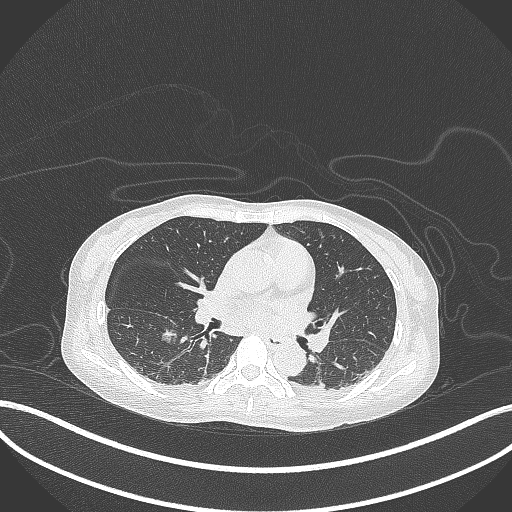
Chest CT, one axial slice. Slice 161 of 261 in the series (ordered by position). Reconstruction kernel B70f. 120 kVp. Lung window (W 1500 / L -600 HU). 1 mm slice thickness. 512 × 512 image matrix. Patient: female, 44 years. Case-level facts recorded for this patient, not image findings: clinical TNM (as recorded): T1c N0 M0.
Outlined on this slice (rectangle marked by the reading radiologist):
- lung tumour (recorded histology: adenocarcinoma): box from (x=156, y=329) to (x=181, y=348) px